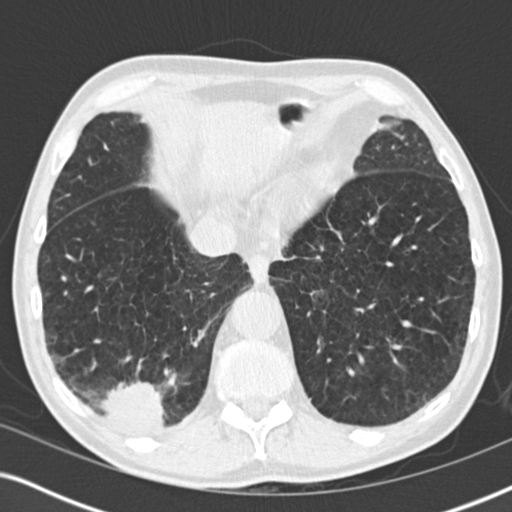
Low-dose screening chest CT, one axial slice; slice 56 of 196 in the series (ordered by position); reconstruction kernel B30f; 120 kVp; lung window (W 1500 / L -600 HU); 2 mm slice thickness; 512 × 512 image matrix, field of view 330 × 330 mm.
Outlined on this slice (manually delineated by an expert):
- lesion 3 (tumor, lower lobe of right lung): bounding box (x1, y1, x2, y2) in pixels: (101, 381, 166, 429)